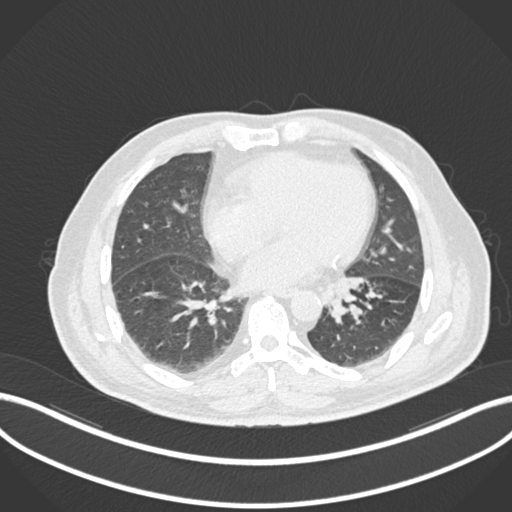
Chest CT, one axial slice. Slice 42 of 161 in the series (ordered by position). Reconstruction kernel B30f. 120 kVp. Lung window (W 1500 / L -600 HU). 1 mm slice thickness. 512 × 512 image matrix, field of view 400 × 400 mm. Patient: male, 71 years. Case-level facts recorded for this patient, not image findings: clinical TNM (as recorded): T1b N0 M0.
Structures marked on this image (rectangle marked by the reading radiologist):
- lung tumour (recorded histology: squamous cell carcinoma): bounding box [x1, y1, x2, y2] px = [319, 271, 368, 324]